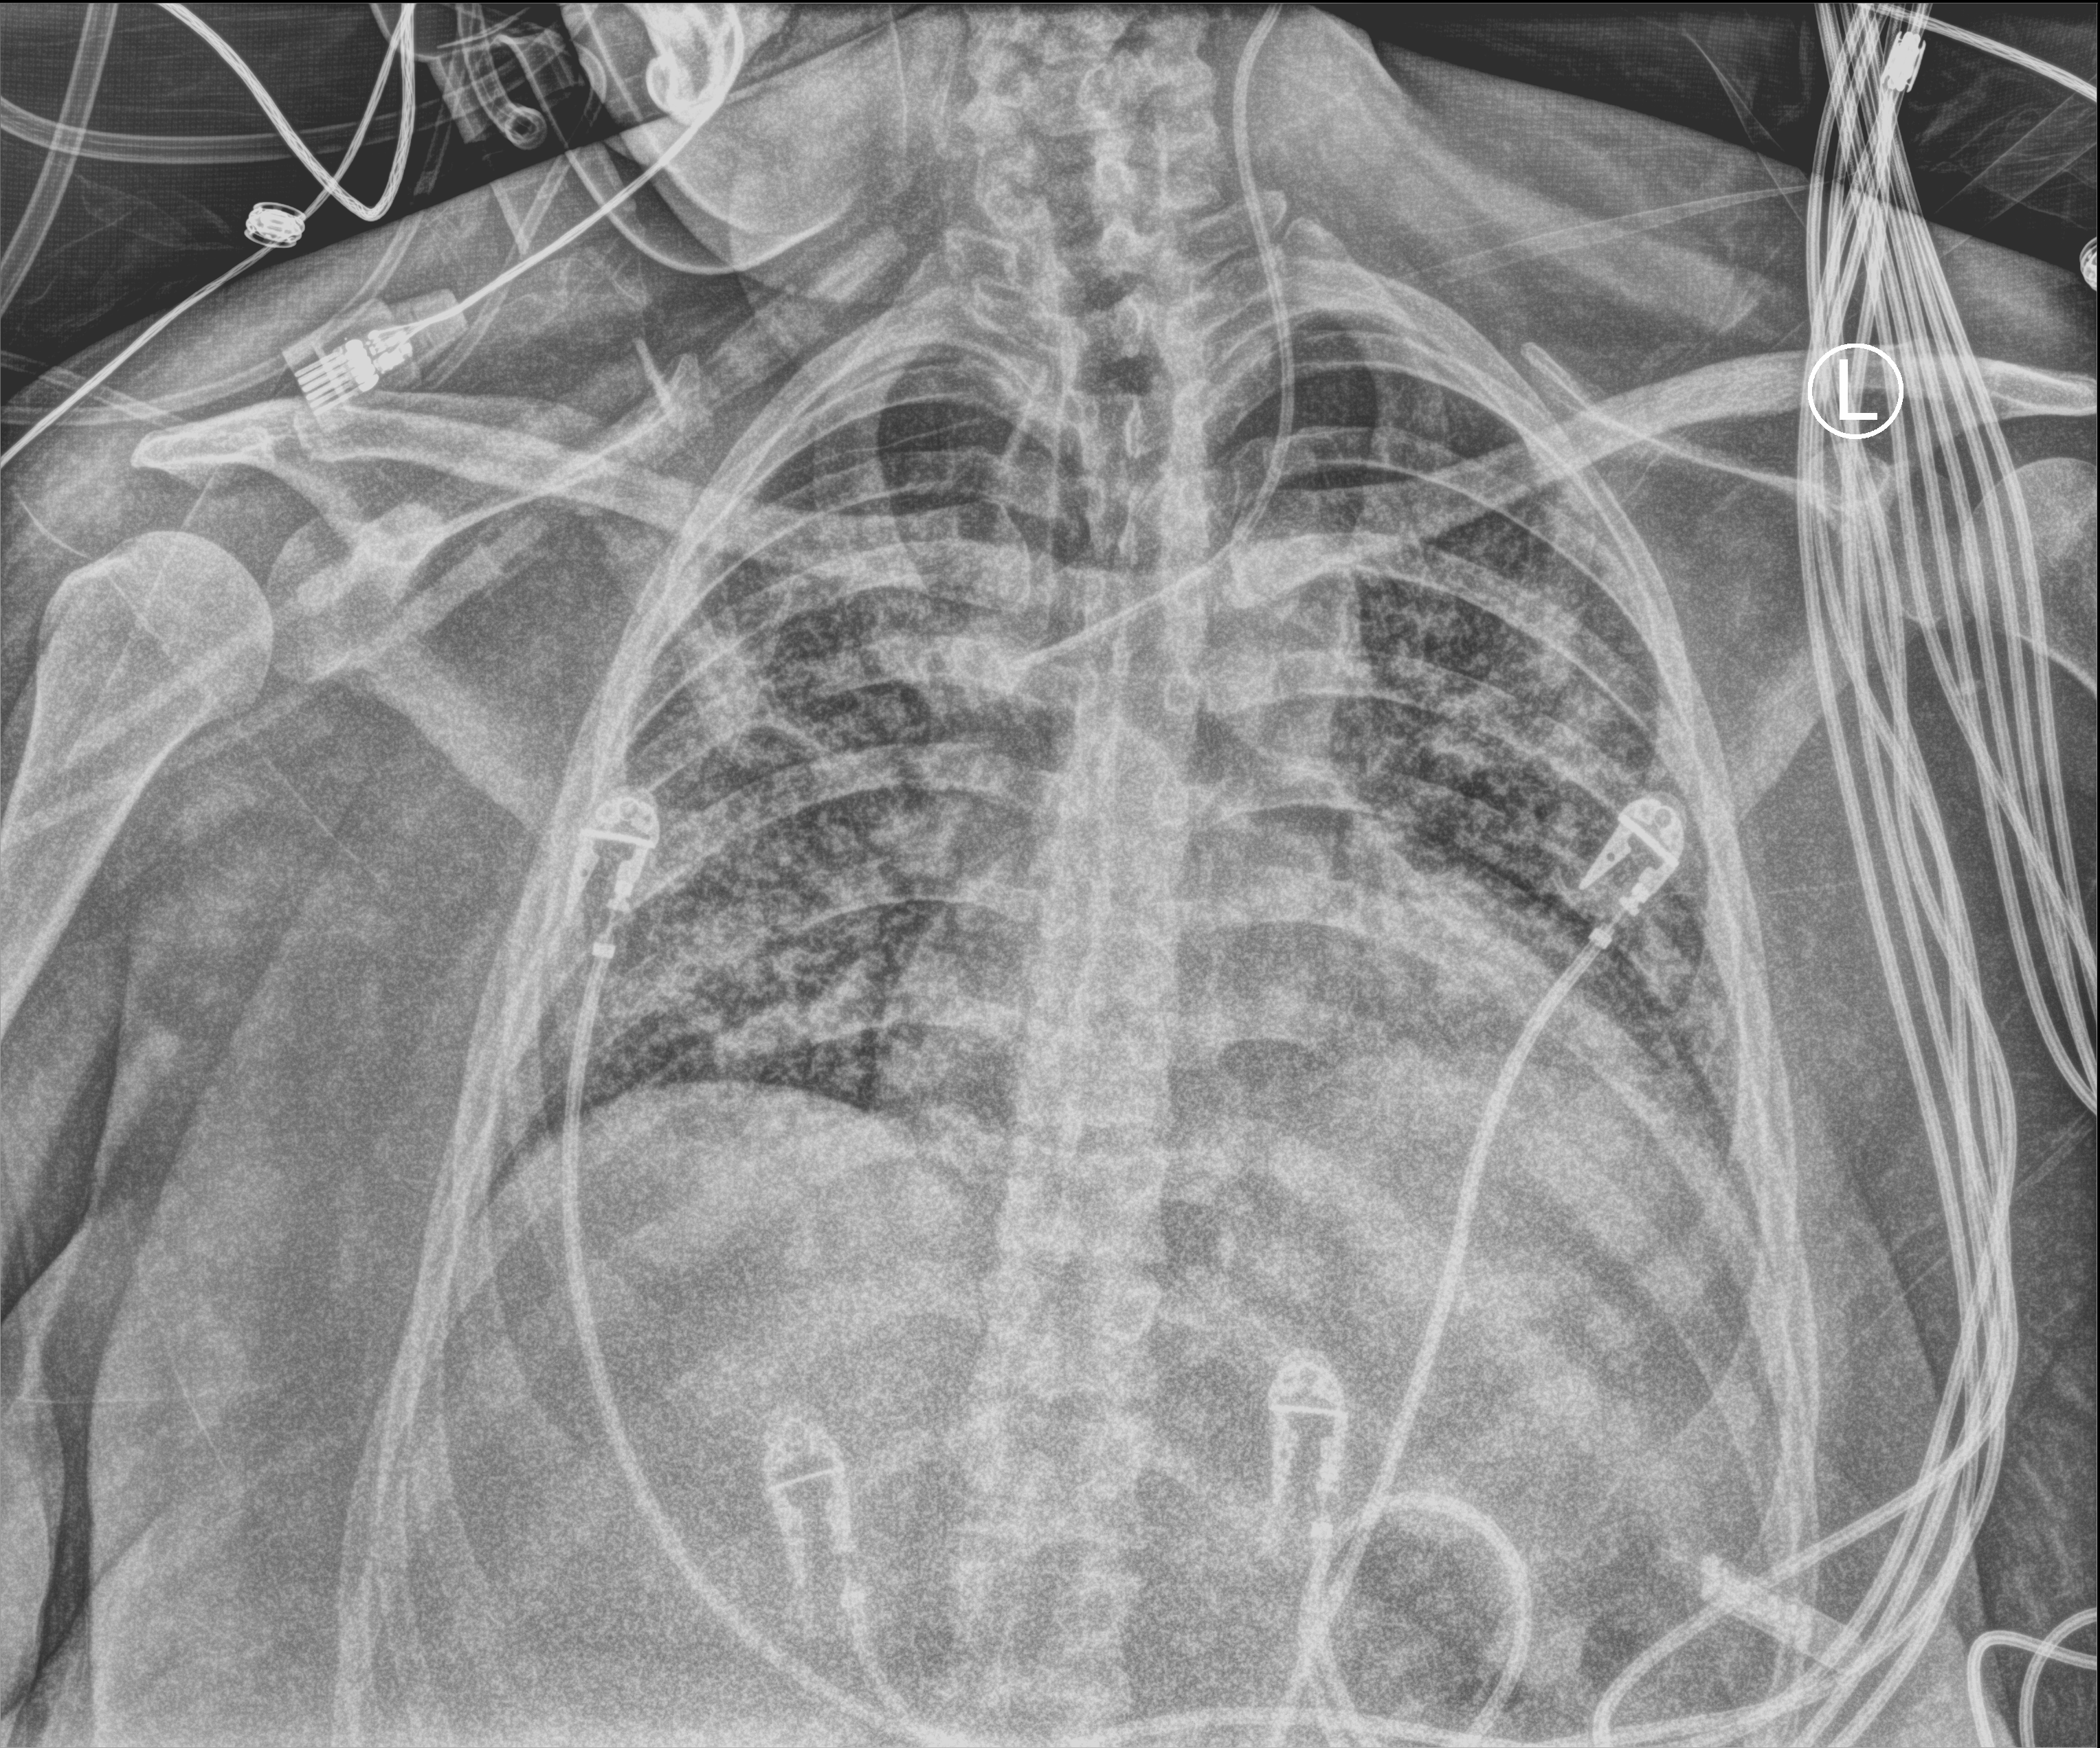
Bedside chest radiograph (computed radiography), anteroposterior (AP) projection. Patient hospitalised with COVID-19; female, aged 18–59 years.
From the hospital-stay record, not from the radiograph (when in the stay this image was taken is not recorded):
- mechanically ventilated during this hospital stay: yes
- admitted to intensive care during this hospital stay: no